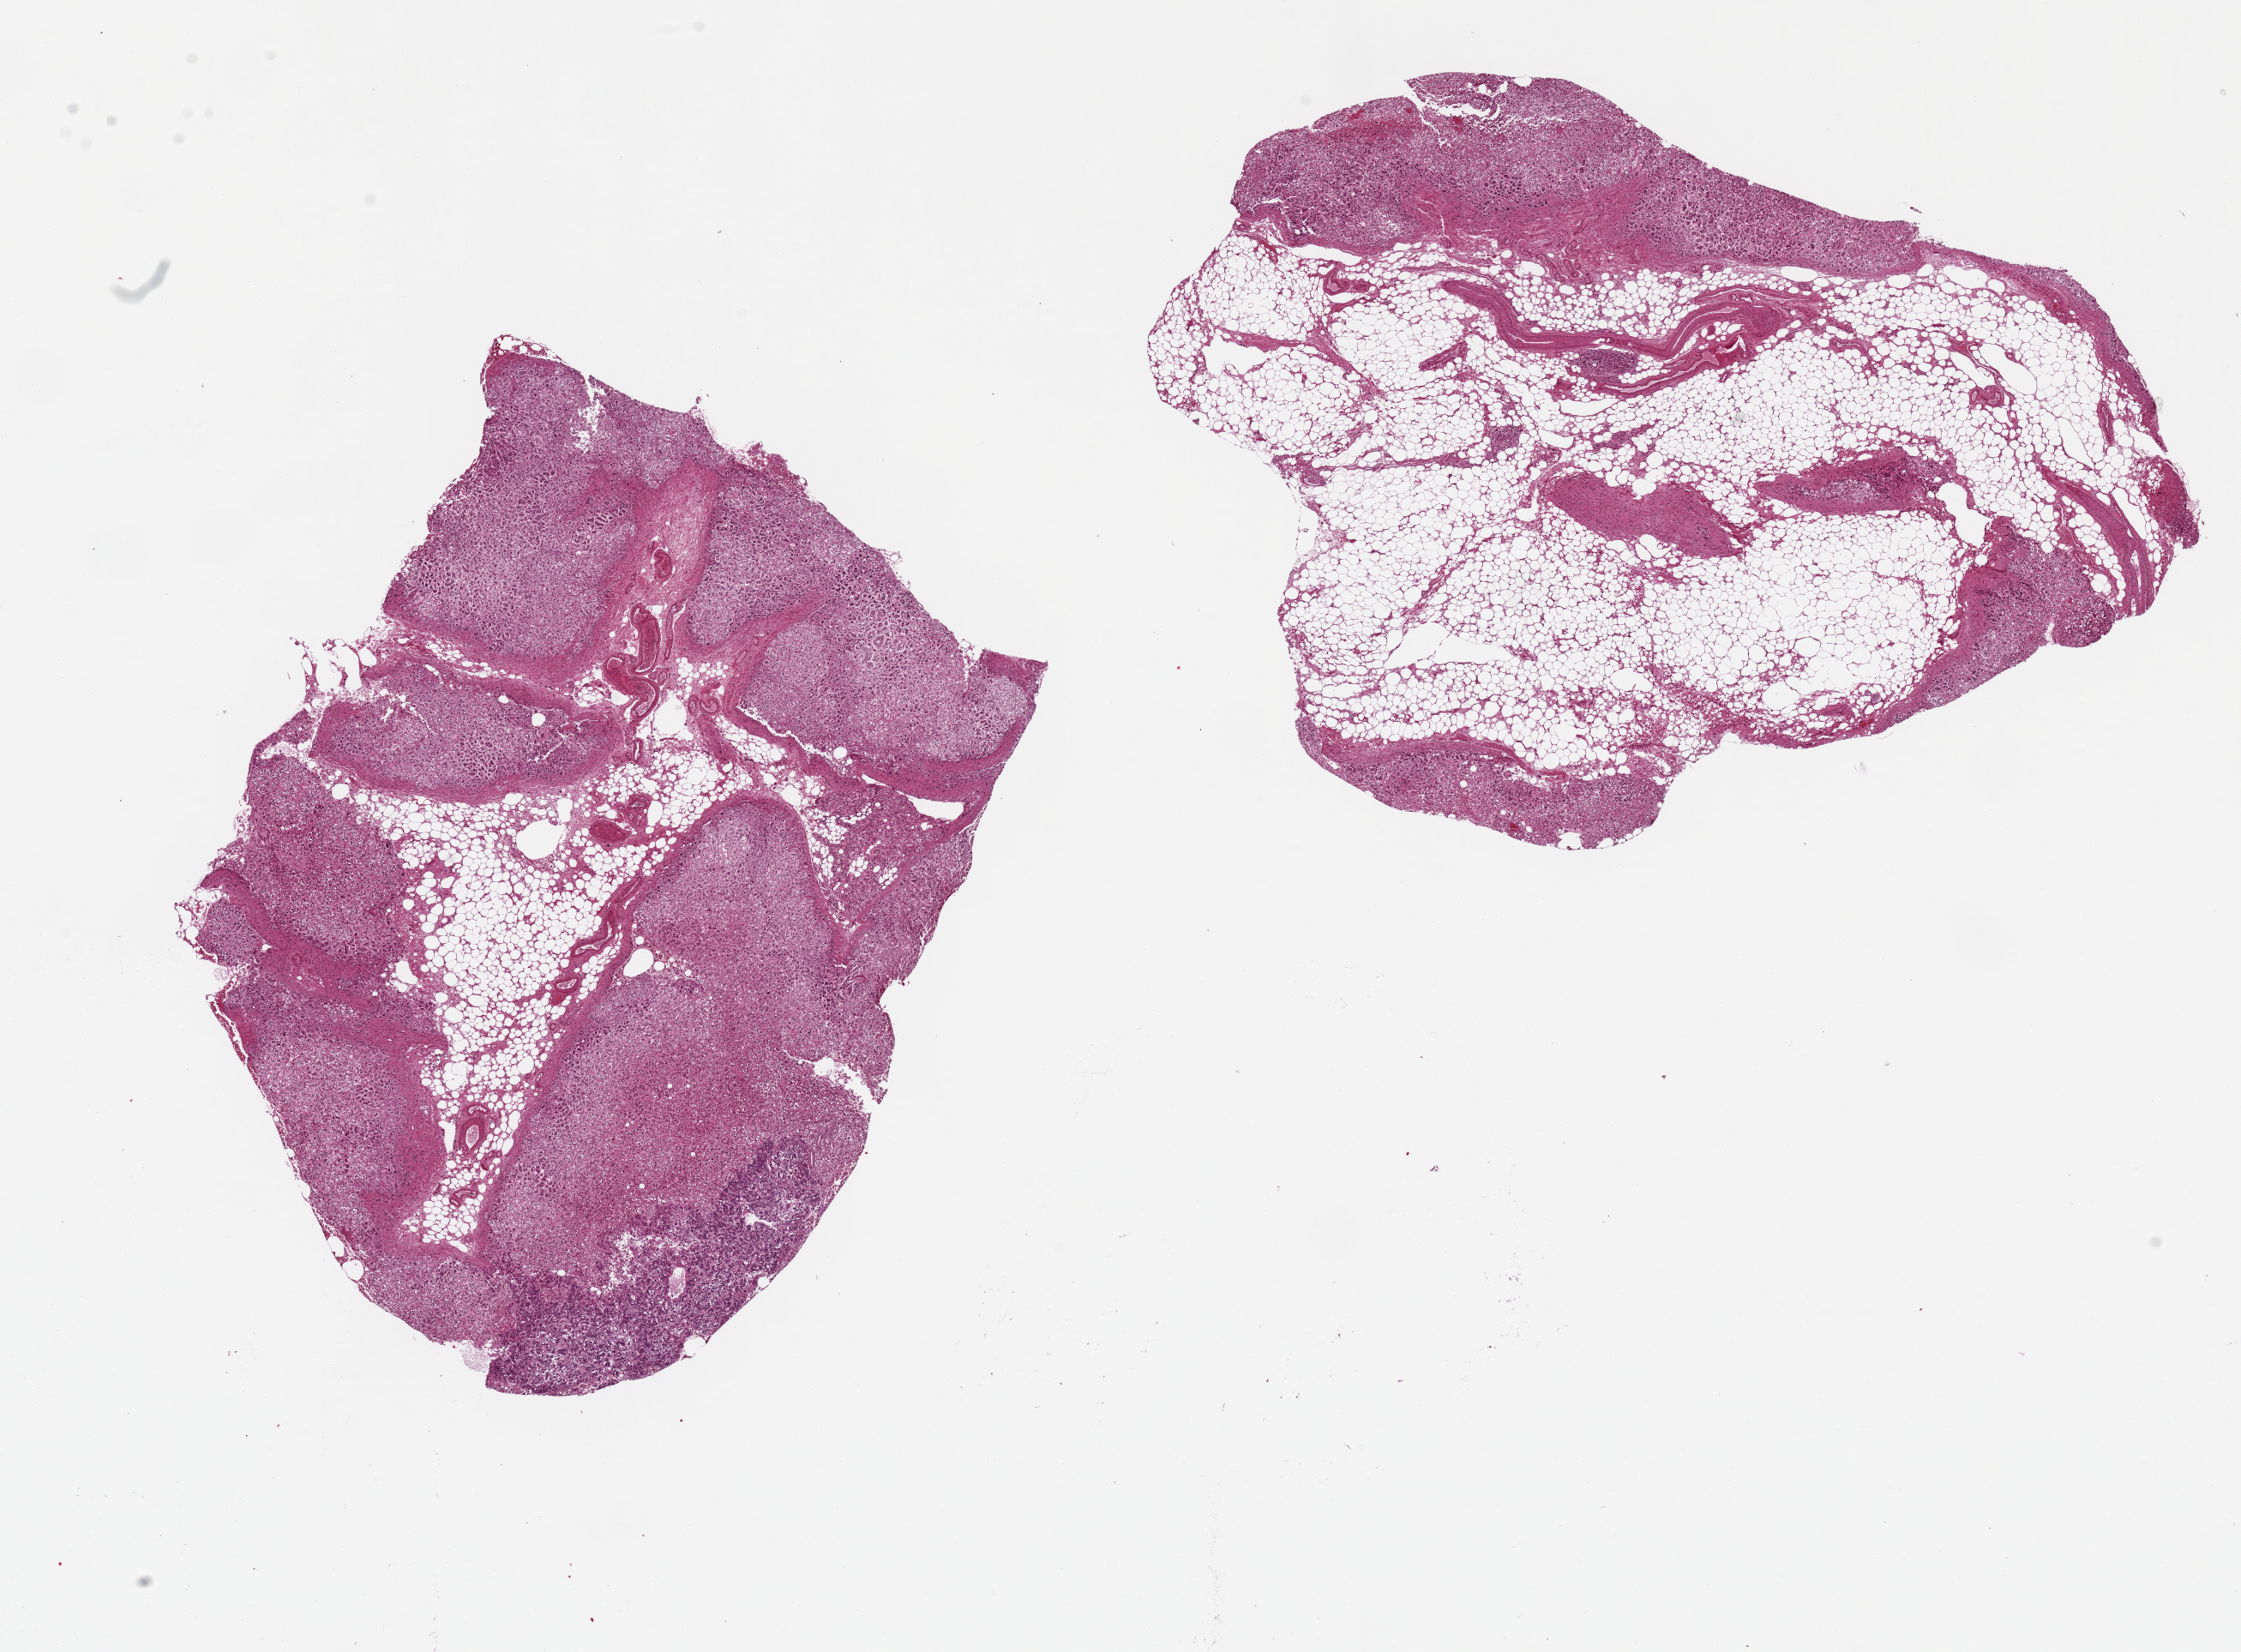
Whole-slide image, haematoxylin and eosin stain — a low-resolution overview of the entire scanned area, about 20.7 x 15.2 mm; PAXgene-fixed paraffin-embedded (PFPE) section; sampled site (target tissue): adrenal gland; tissue donor sample.
• pathologist's review note for this sample: 2 pieces, 9x7 & 9x7mm; ~50-60% interstitial/adherent fat, badly autolyzed